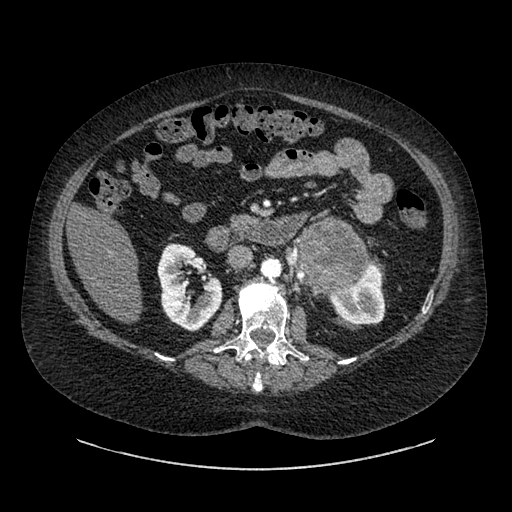
Contrast-enhanced abdominal CT, one axial slice. Position 512 of 769 along the scan axis. 120 kVp. Intravenous contrast given. Soft-tissue window (W 400 / L 40 HU). 512 × 512 image matrix, field of view 460 × 460 mm. Patient: female, 61 years. From the clinical record (not read from this slice): diagnosis: adrenocortical carcinoma; tumour side: left adrenal; tumour size at pathology: 13 cm; Ki-67 index: 79 %.
Annotated regions visible in this slice (semi-automatic segmentation, software-assisted and operator-edited):
- mass: box from (x=299, y=223) to (x=368, y=287) px